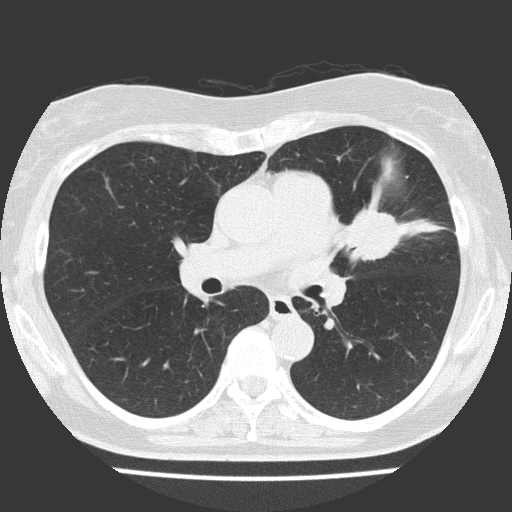
Low-dose screening chest CT, one axial slice. 120 kVp. Lung window (W 1500 / L -600 HU). 2 mm slice thickness. 512 × 512 image matrix.
Structures marked on this image (outlined manually by an expert reader):
- lesion 1 (tumor, upper lobe of left lung): bounding box (x1, y1, x2, y2) in pixels: (345, 206, 402, 261)